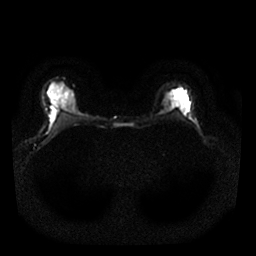
Breast MRI, one axial slice; slice 20 of 25 in the series (ordered by position); diffusion-weighted series; image 2 of 4 stored at this slice position (different b-values; order by instance number); 1.5 T; 4 mm slice thickness; 256 × 256 image matrix. Female patient.
Outlined on this slice (expert manual segmentation):
- tumour on diffusion-weighted imaging: box from (x=164, y=106) to (x=169, y=111) px